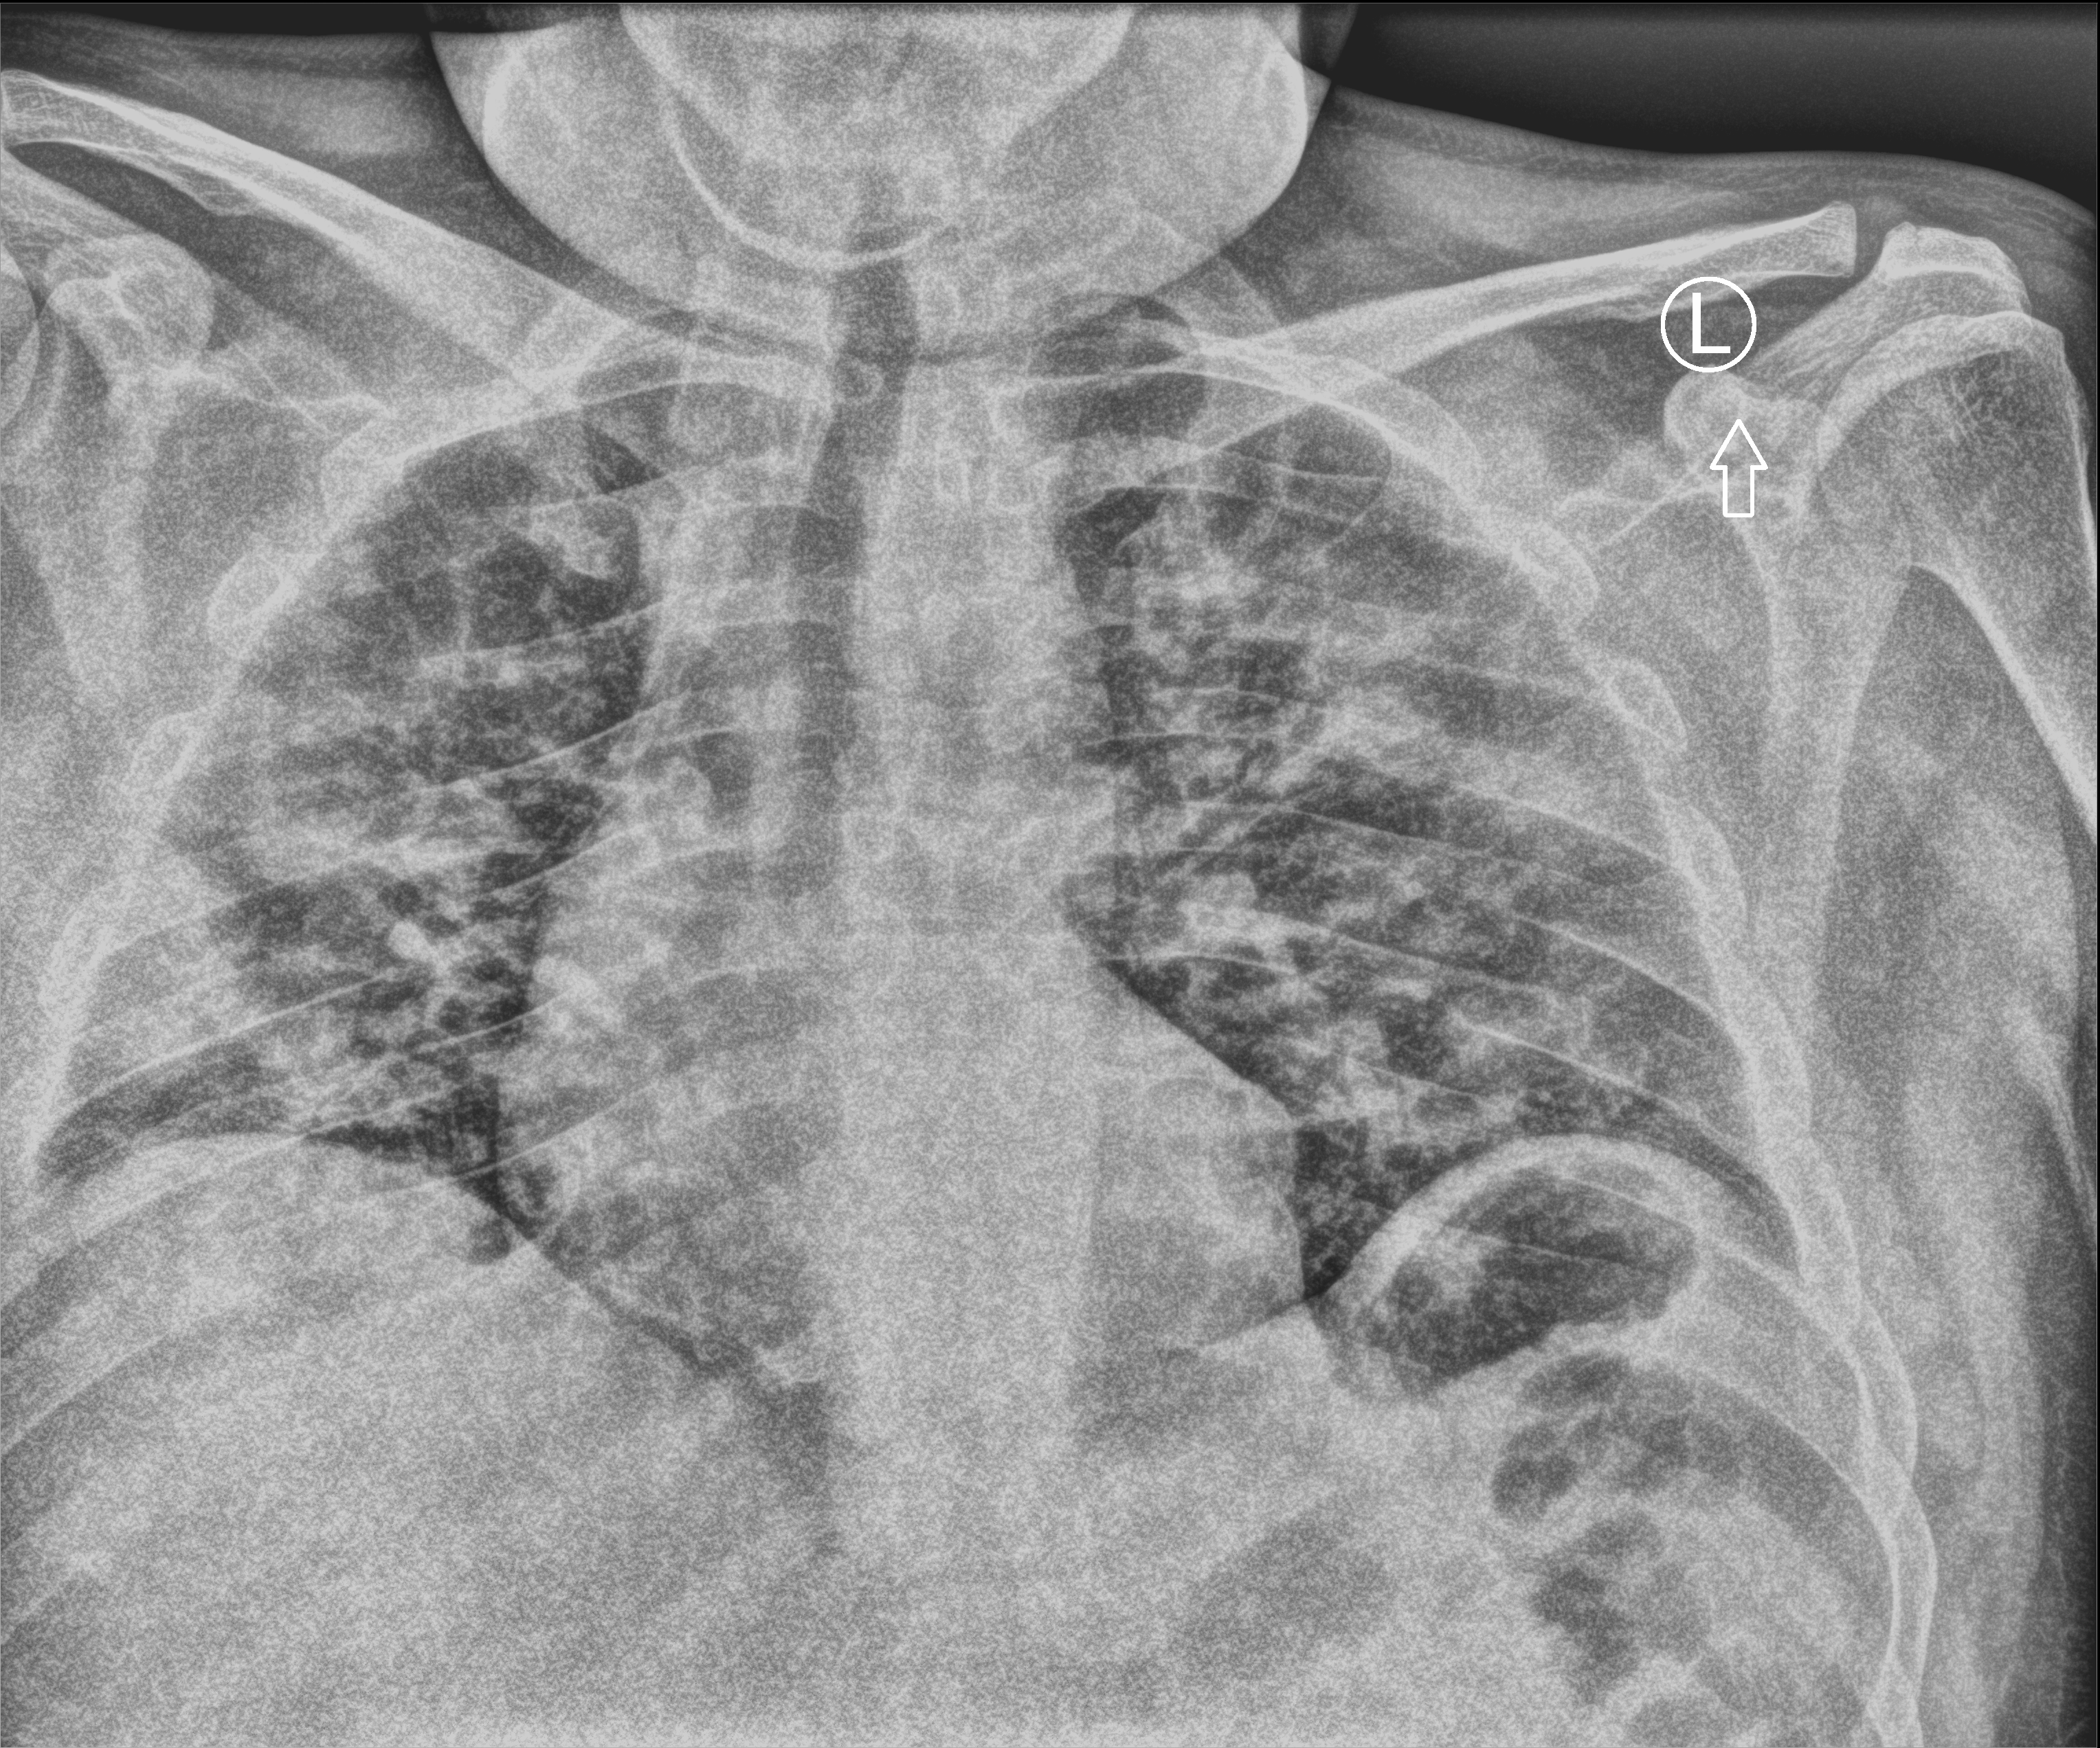
Portable chest radiograph; anteroposterior (AP) projection. Patient hospitalised with COVID-19; female, aged 18–59 years.
Hospital-stay facts (about this admission, not read from this image; timing relative to this image not recorded):
- mechanically ventilated during this hospital stay: yes